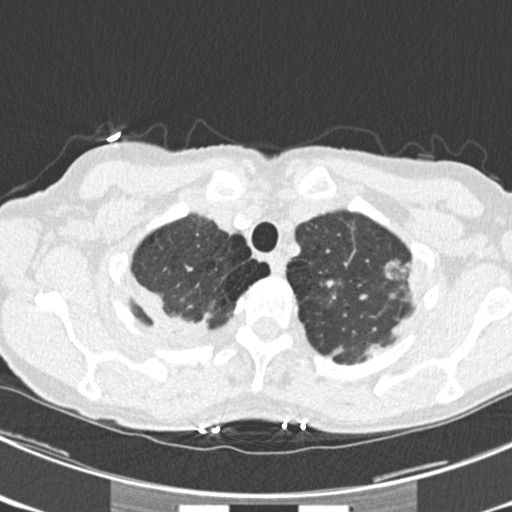
Axial slice from a low-dose chest CT screening exam; third screening round (two years after baseline); lung window (W 1500 / L -600 HU); 2 mm slice thickness; standard (soft-tissue) reconstruction kernel (B30f); 120 kVp; slice 36 of 225 in the series; 512 × 512 image matrix. Female, age 63 years at enrolment.
Lesion marked by an expert reader, bounding box <370,247,435,311> (left, top, right, bottom; pixels). The screening reader recorded 9 non-calcified nodules or masses ≥4 mm on this exam (left upper lobe, right upper lobe, left upper lobe, left lower lobe, right middle lobe, left lower lobe, left lower lobe, right lower lobe, right lower lobe); which of them this box marks is not recorded. Official screen result: positive, other. Later outcome: lung cancer diagnosed 15 days after this screen — bronchiolo-alveolar adenocarcinoma, NOS, right upper lobe, right middle lobe, right lower lobe, left upper lobe, left lower lobe, moderately differentiated (G2), stage IV (AJCC 6th edition).